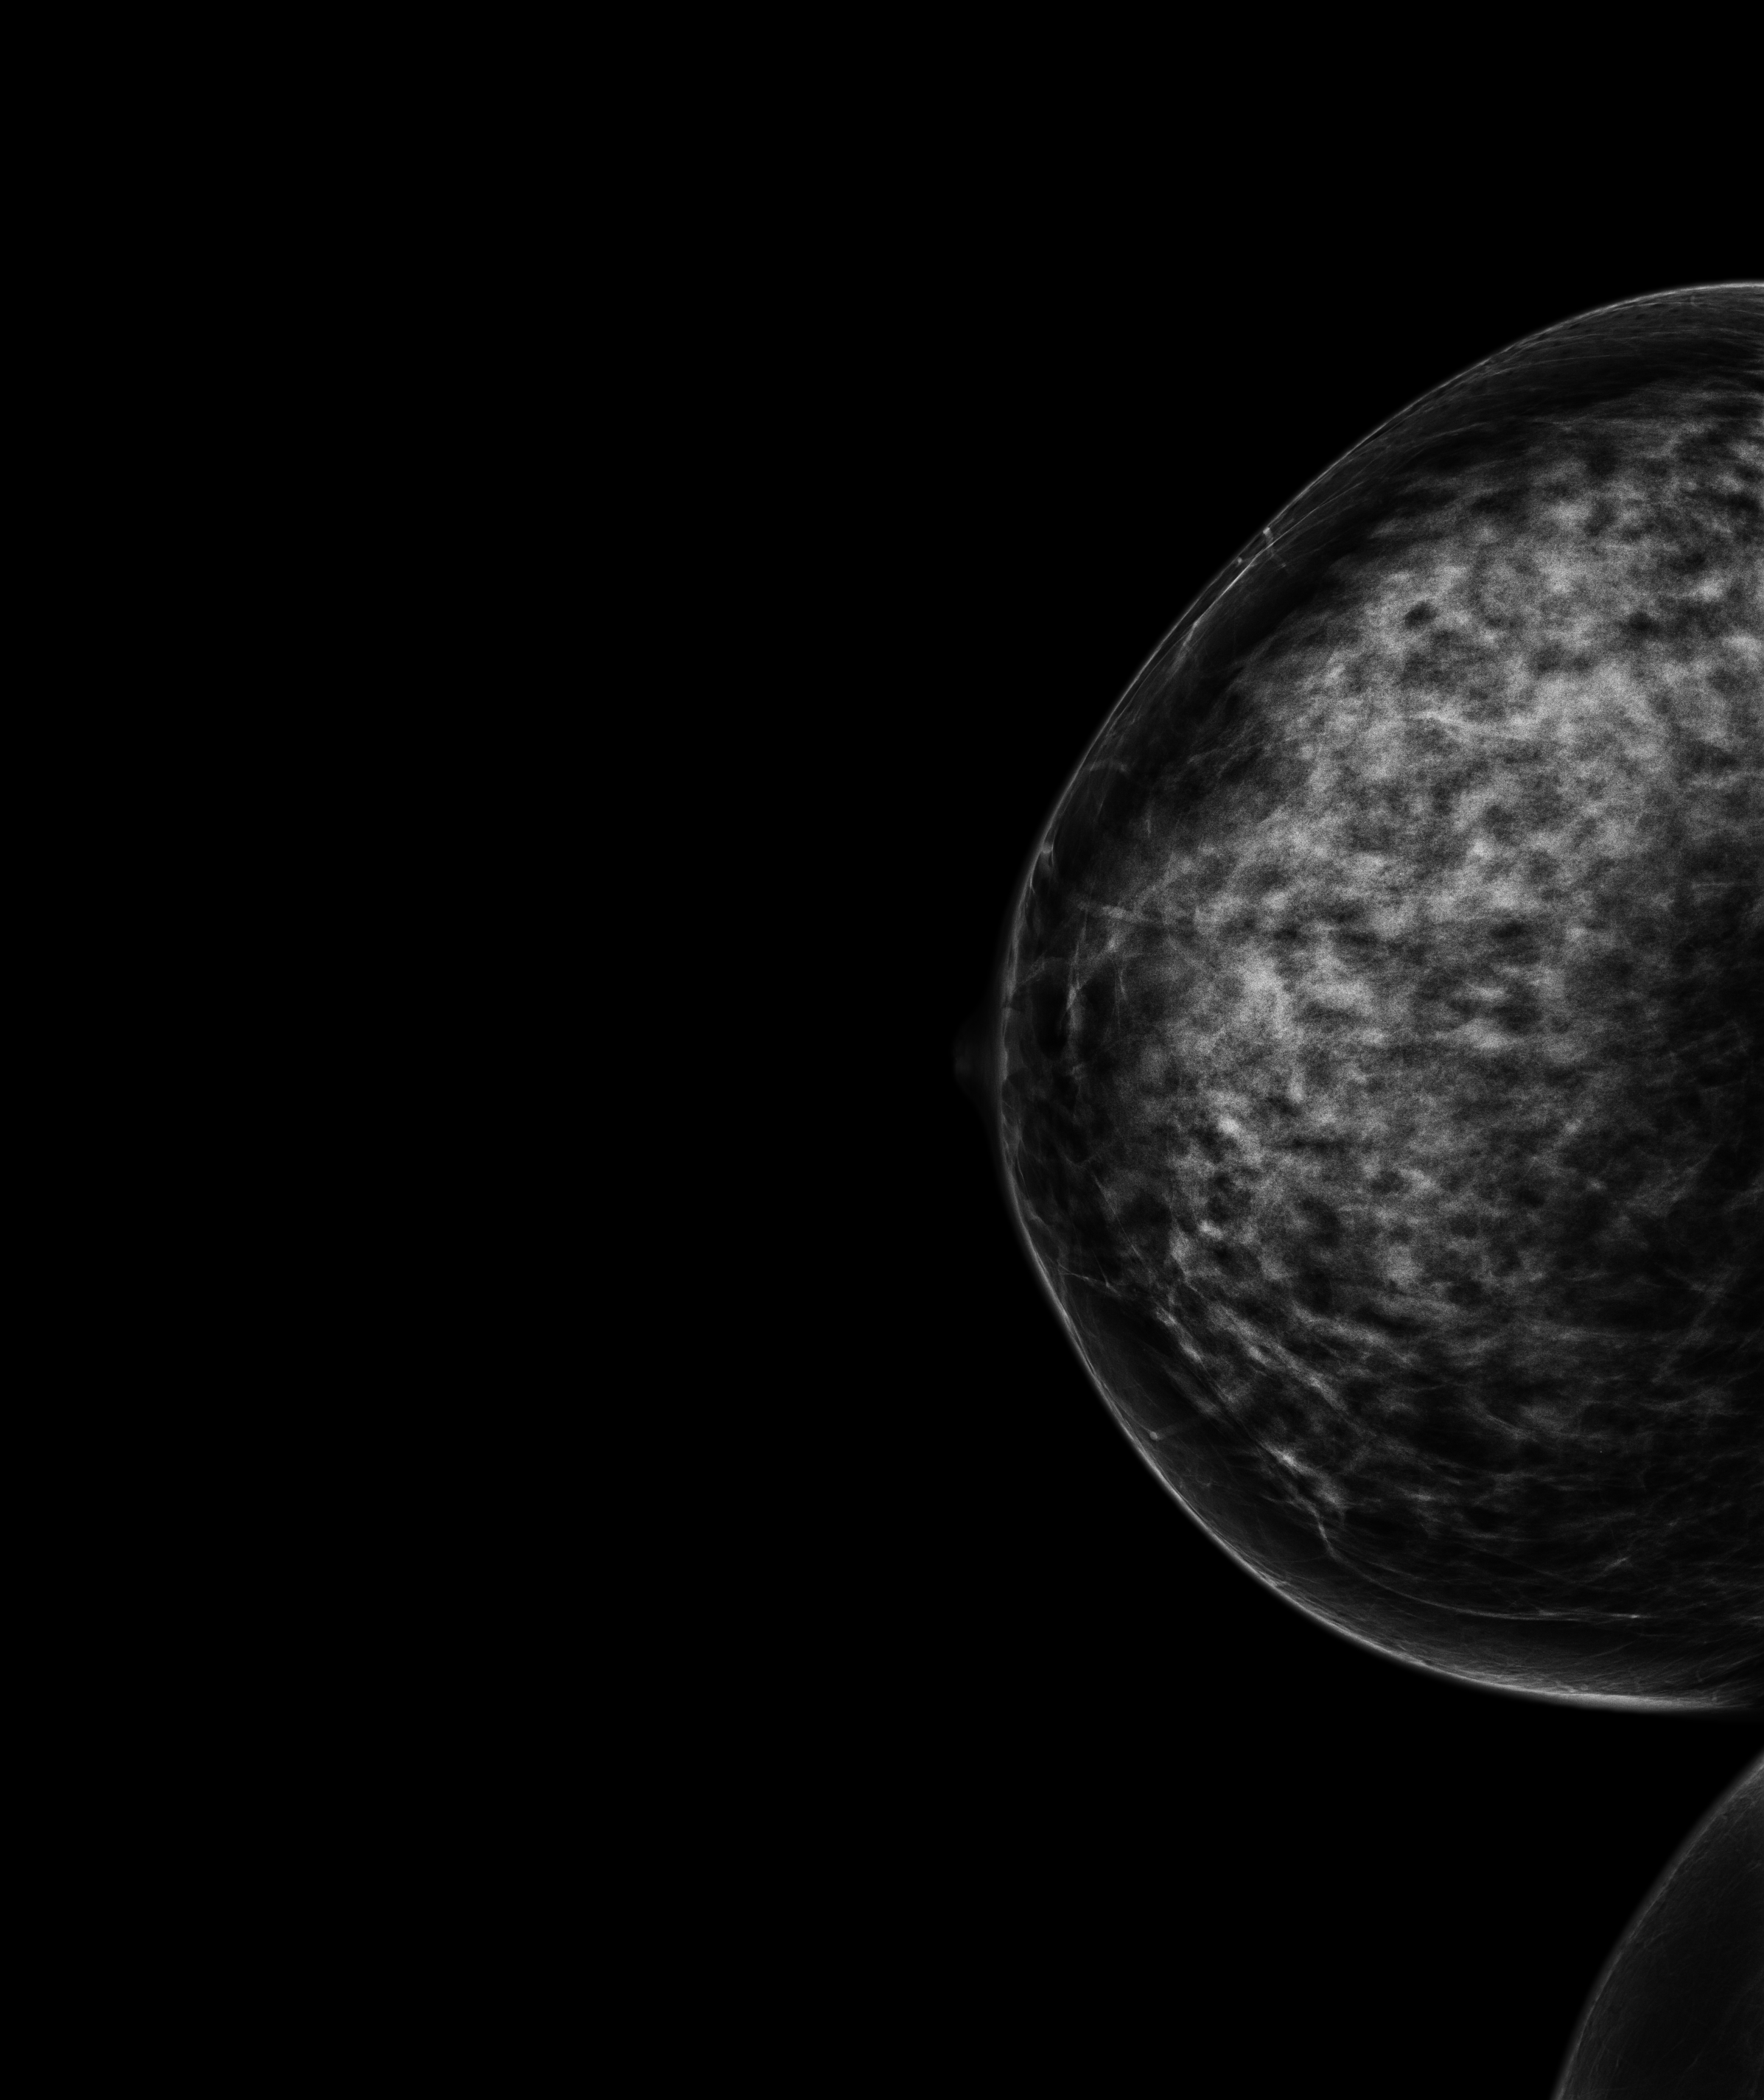
Full-field digital mammogram (FFDM), right breast, CC view, annual screening mammography examination, compressed breast thickness 59.2 mm, system: Senographe Pristina. Patient aged 42 years (female).
- breast density at the screening exam (both breasts): extremely dense (BI-RADS density category d)
- final BI-RADS assessment for this screening round (tomosynthesis exam, both breasts): category 1
- recall: no recall after this screen